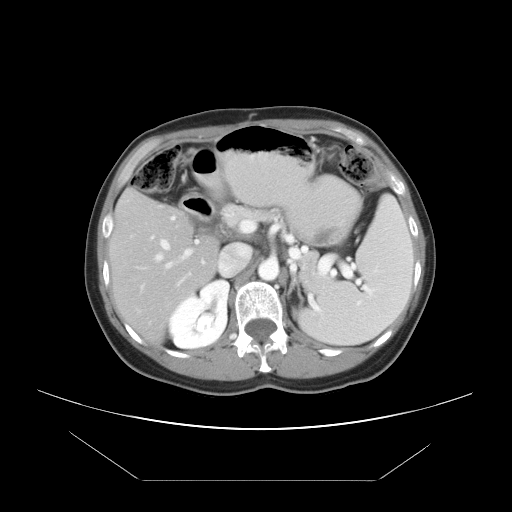
Contrast-enhanced abdominal CT, one axial slice. Position 26 of 45 along the scan axis. Soft-tissue window (W 400 / L 40 HU). 5 mm slice thickness. 512 × 512 image matrix, field of view 405 × 405 mm. Female patient, age 52 years. From the clinical record (not read from this slice): diagnosis: colorectal cancer liver metastases, imaged before liver resection; multiple liver metastases: yes; largest metastasis: 2.5 cm.
Structures marked on this image (manually delineated by an expert):
- hepatic veins: bounding box (x1, y1, x2, y2) in pixels: (156, 240, 172, 267)
- liver: (112, 192, 219, 339)
- planned liver remnant (the part of the liver to remain after resection): (112, 192, 219, 338)
- portal vein (with intrahepatic branches): (150, 215, 199, 275)